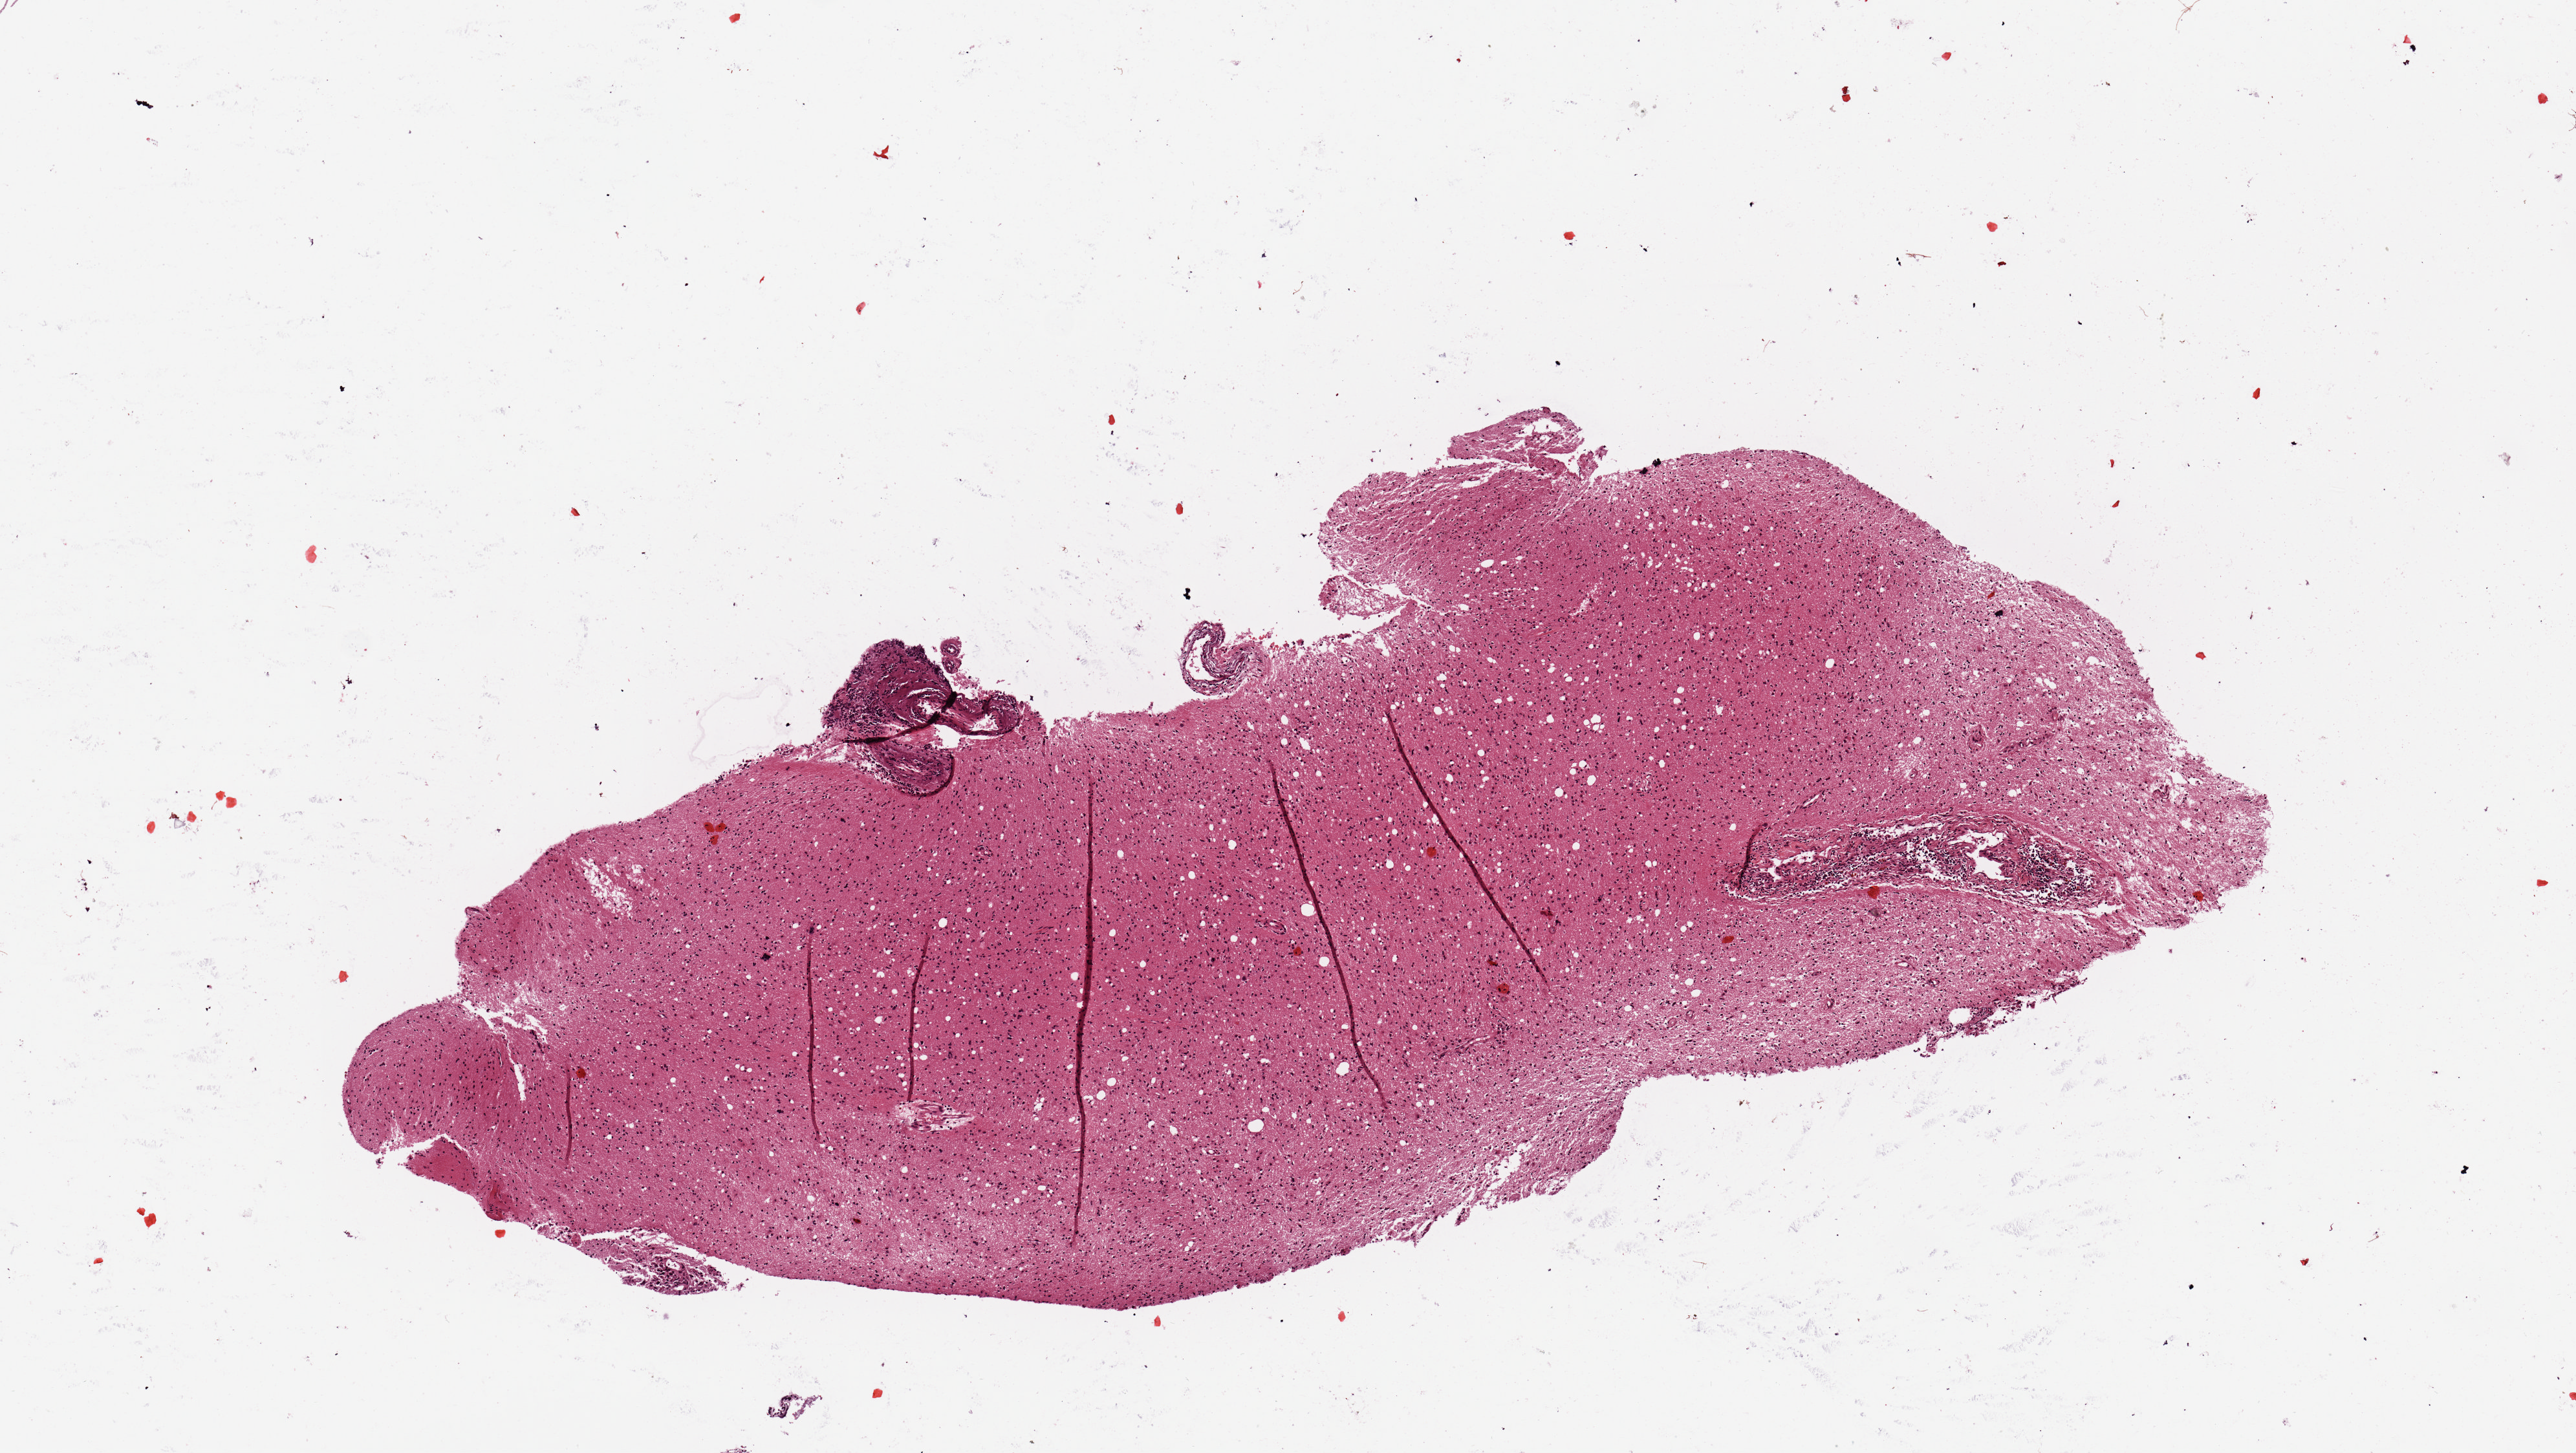
Whole-slide histology image, H&E-stained — a low-resolution overview of the entire scanned area, about 7.9 x 4.4 mm, brain, tumour tissue. 63-year-old female patient.
Histologic diagnosis: Glioblastoma. Primary tumour site (as recorded): temporal lobe.